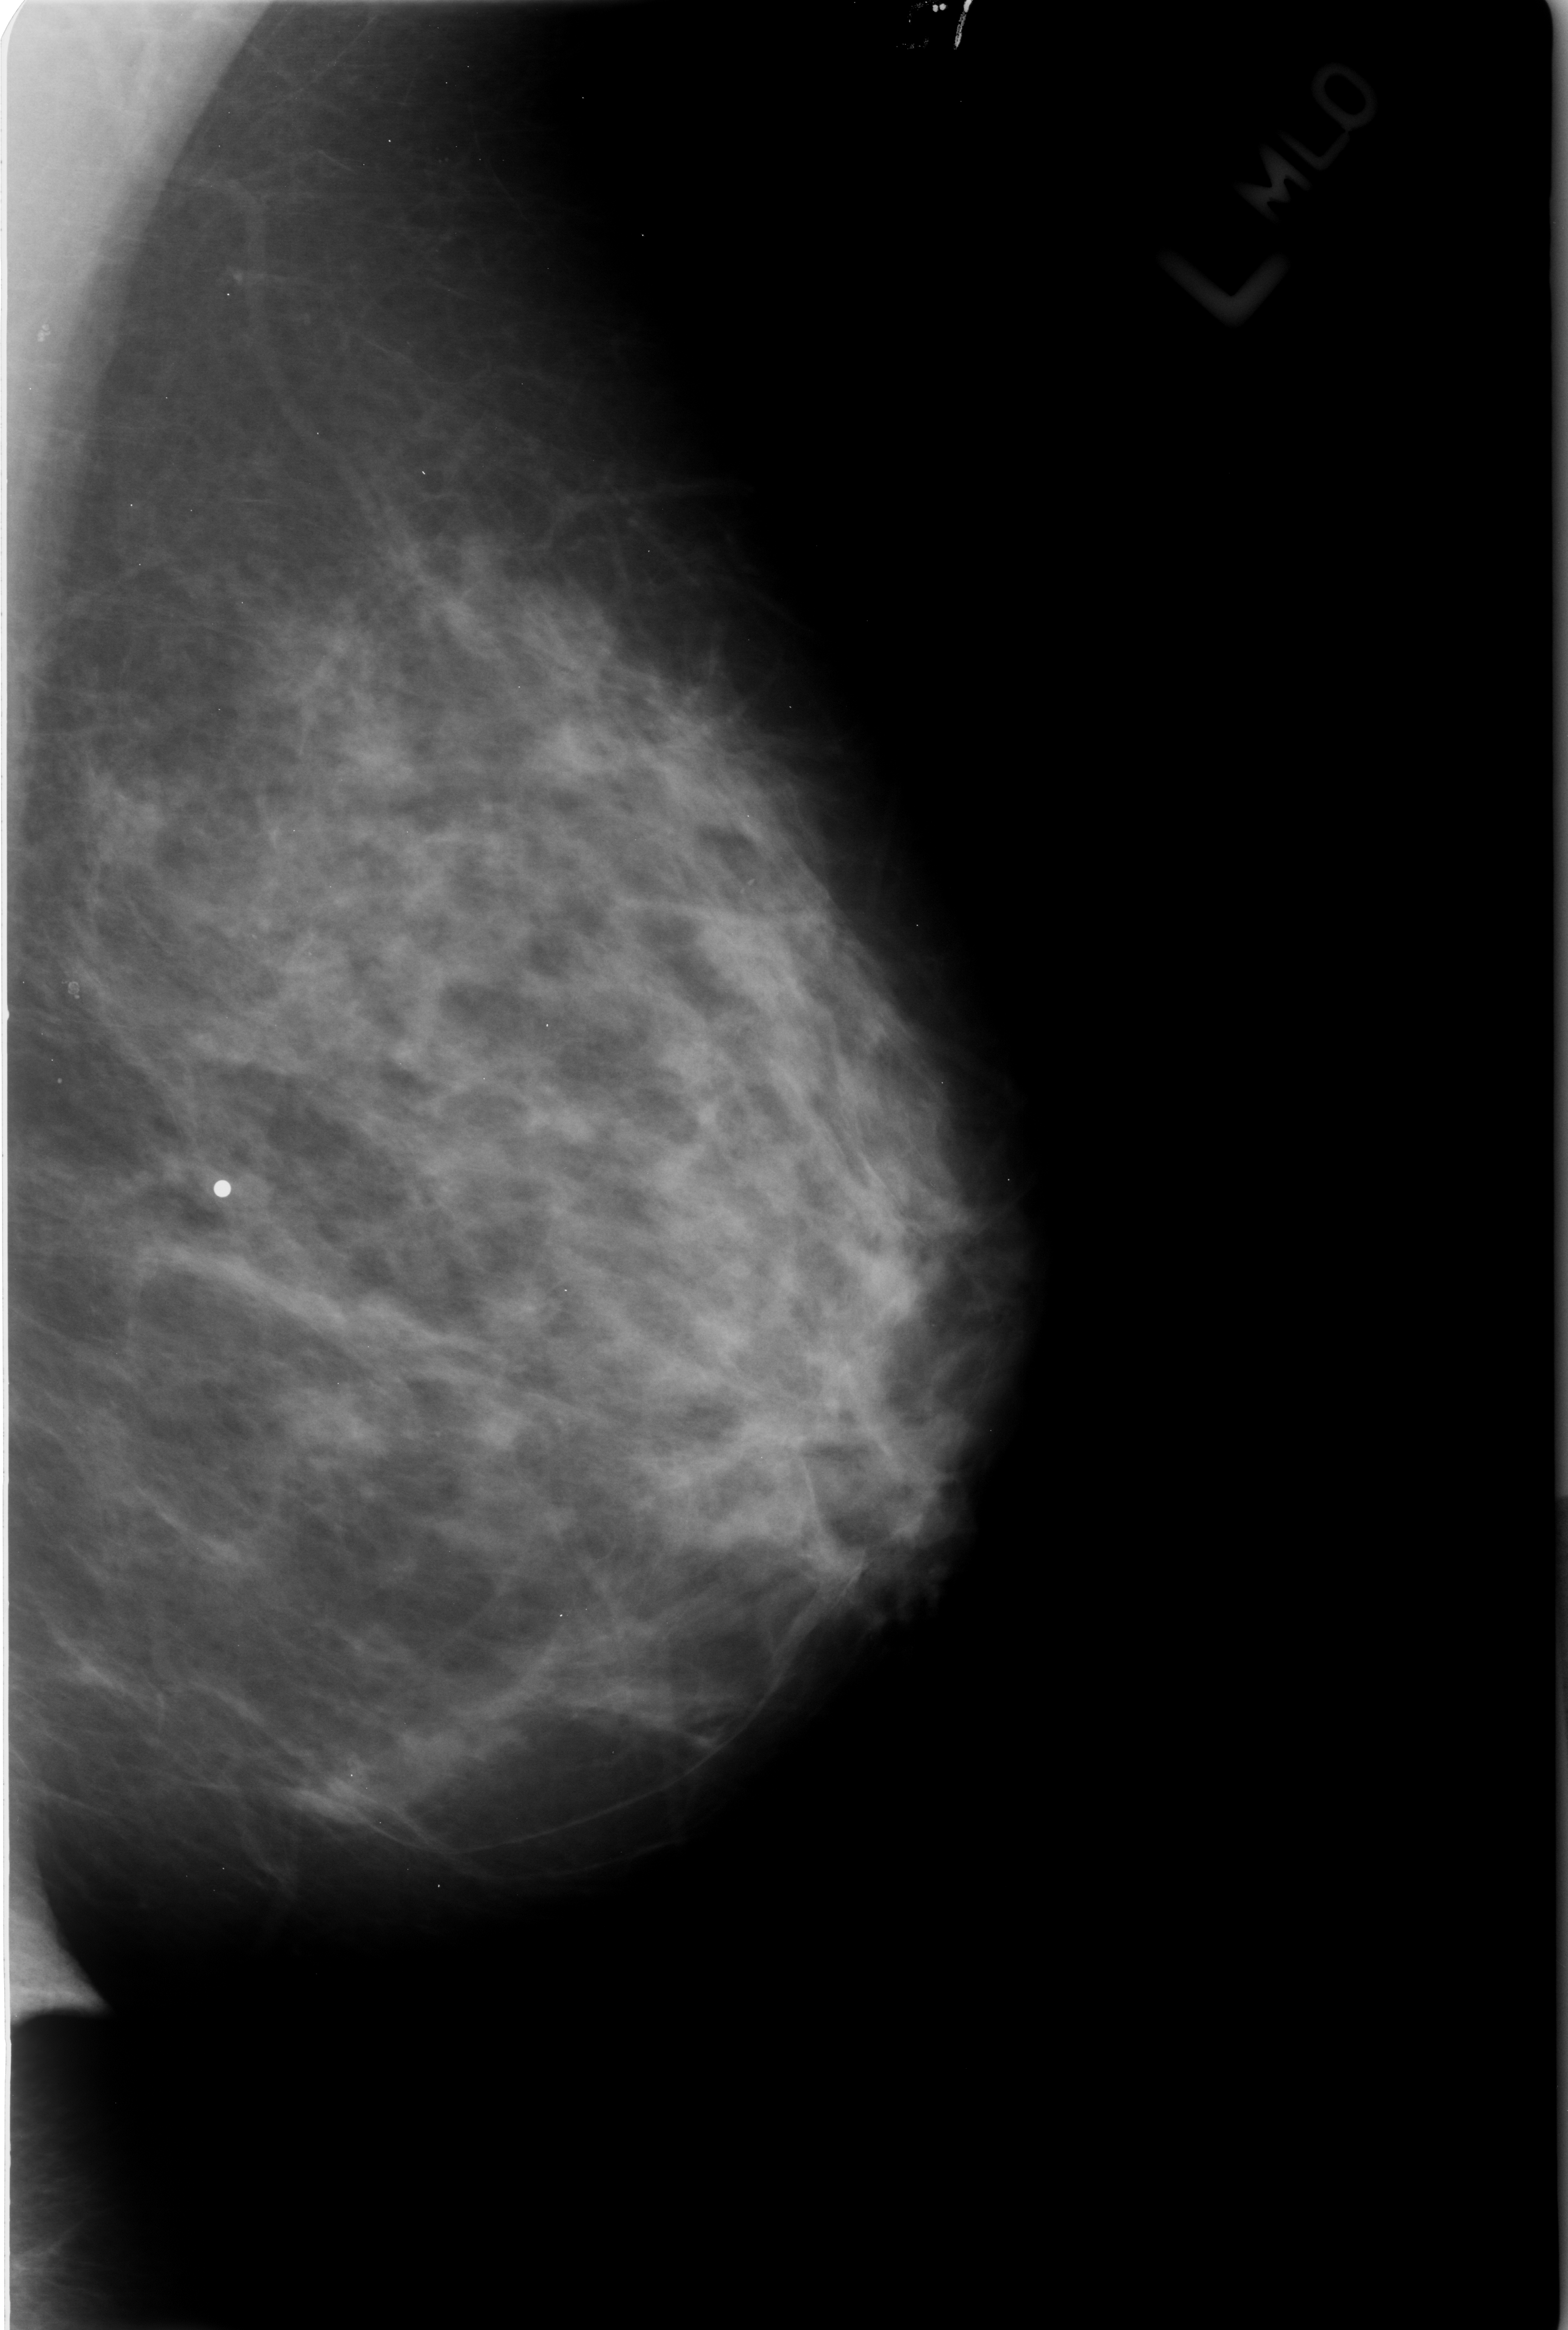
Scanned film-screen mammogram. Left breast. MLO view. BI-RADS breast density category 3 (scale 1–4). 1568 × 2330 image matrix.
Marked abnormalities (boxes around the expert regions of interest):
- calcifications, morphology lucent center; BI-RADS assessment category 2; subtlety rating 3 on a 1 (subtle) to 5 (obvious) scale; benign; no additional work-up was recommended (outcome (as recorded, no biopsy): benign without callback): bounding box [x1, y1, x2, y2] px = [209, 1169, 244, 1207]